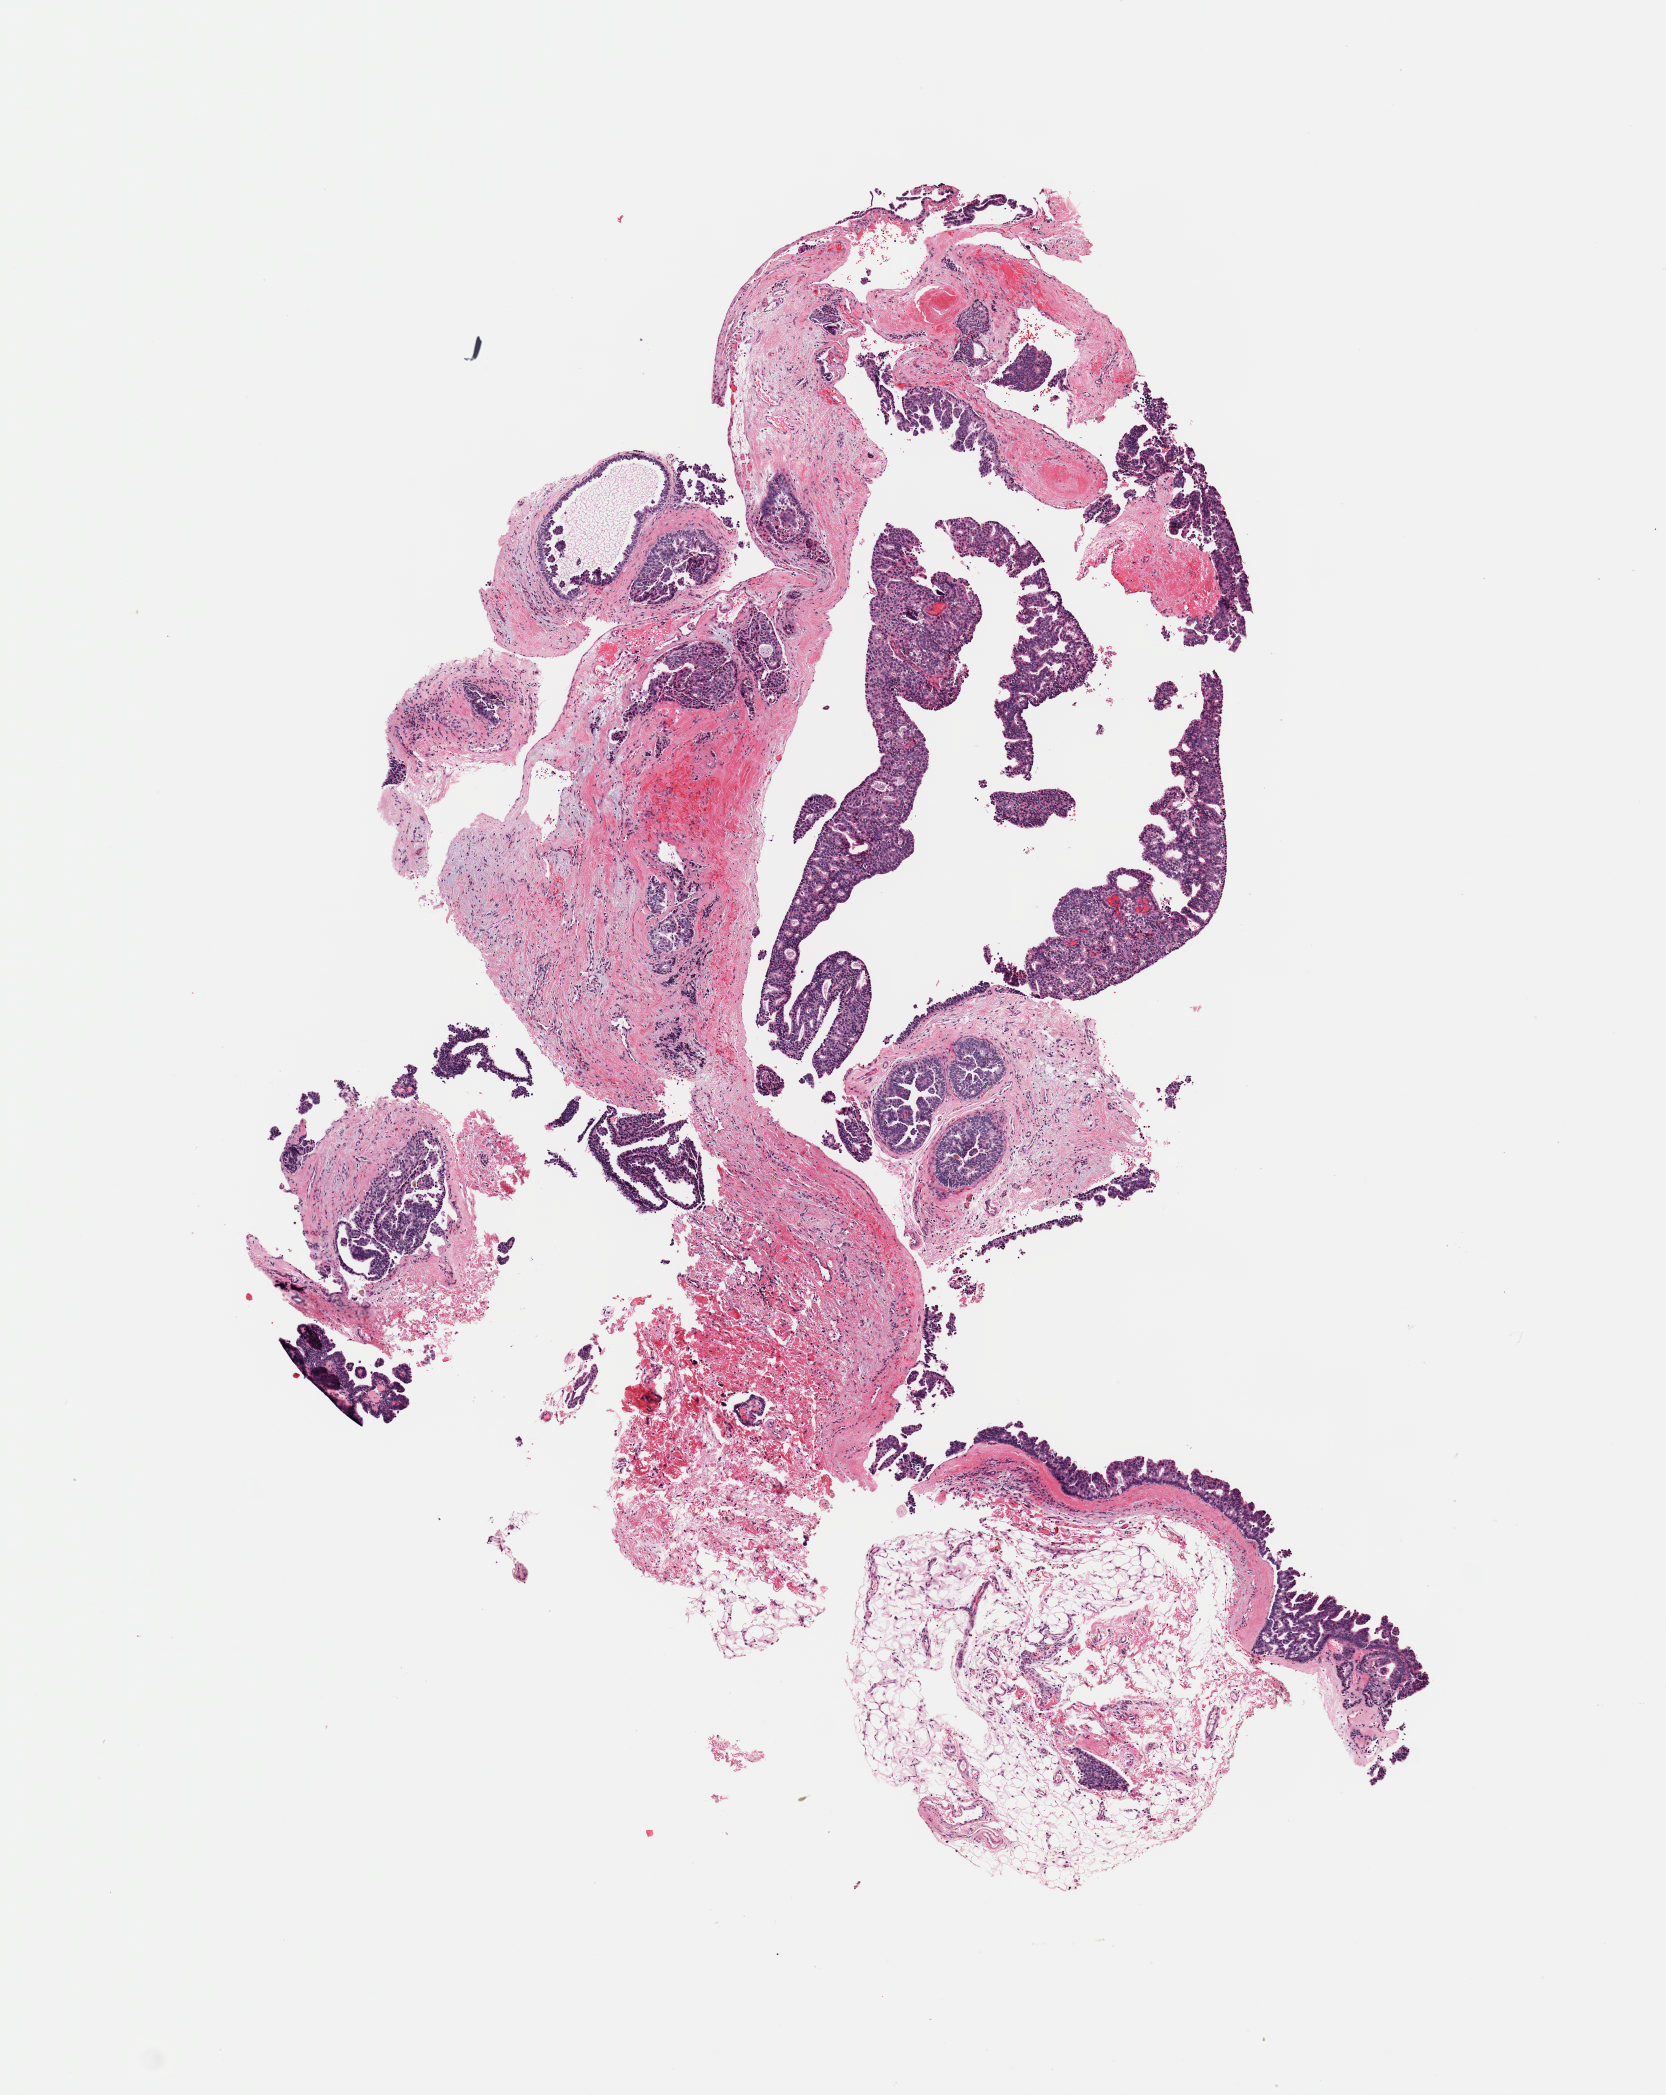
Whole-slide histology image, H&E, a low-resolution overview of the entire scanned area, about 6.6 x 8.3 mm, frozen section from the bottom of the tissue portion, sample: primary tumour, breast. Patient: female, age at initial diagnosis 63 years.
Histologic diagnosis: Infiltrating duct carcinoma, NOS.